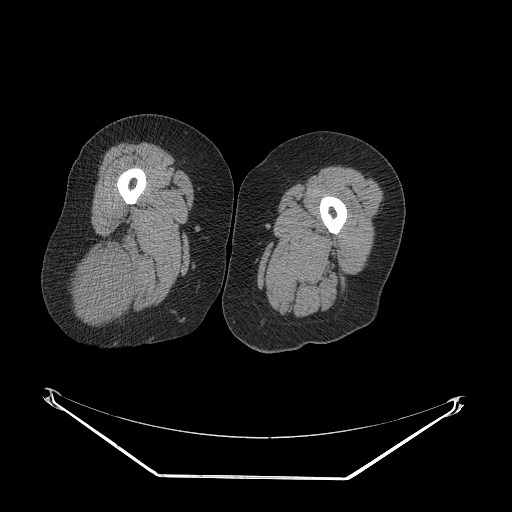
CT of an extremity soft-tissue mass (from a PET/CT study), one axial slice. Slice 30 of 257 in the series (ordered by position). Reconstruction kernel STANDARD. 140 kVp. Soft-tissue window (W 400 / L 40 HU). 512 × 512 image matrix, field of view 500 × 500 mm. Female patient. From the clinical record (not read from this slice): histological type: synovial sarcoma; grade: intermediate; site of the primary tumour: right buttock.
Annotated regions visible in this slice (expert contour drawn on MRI and transferred to this co-registered scan by the dataset authors):
- gross tumour volume including surrounding oedema: box from (x=73, y=242) to (x=133, y=316) px
- gross tumour volume (mass): (x=78, y=249)–(x=133, y=312)